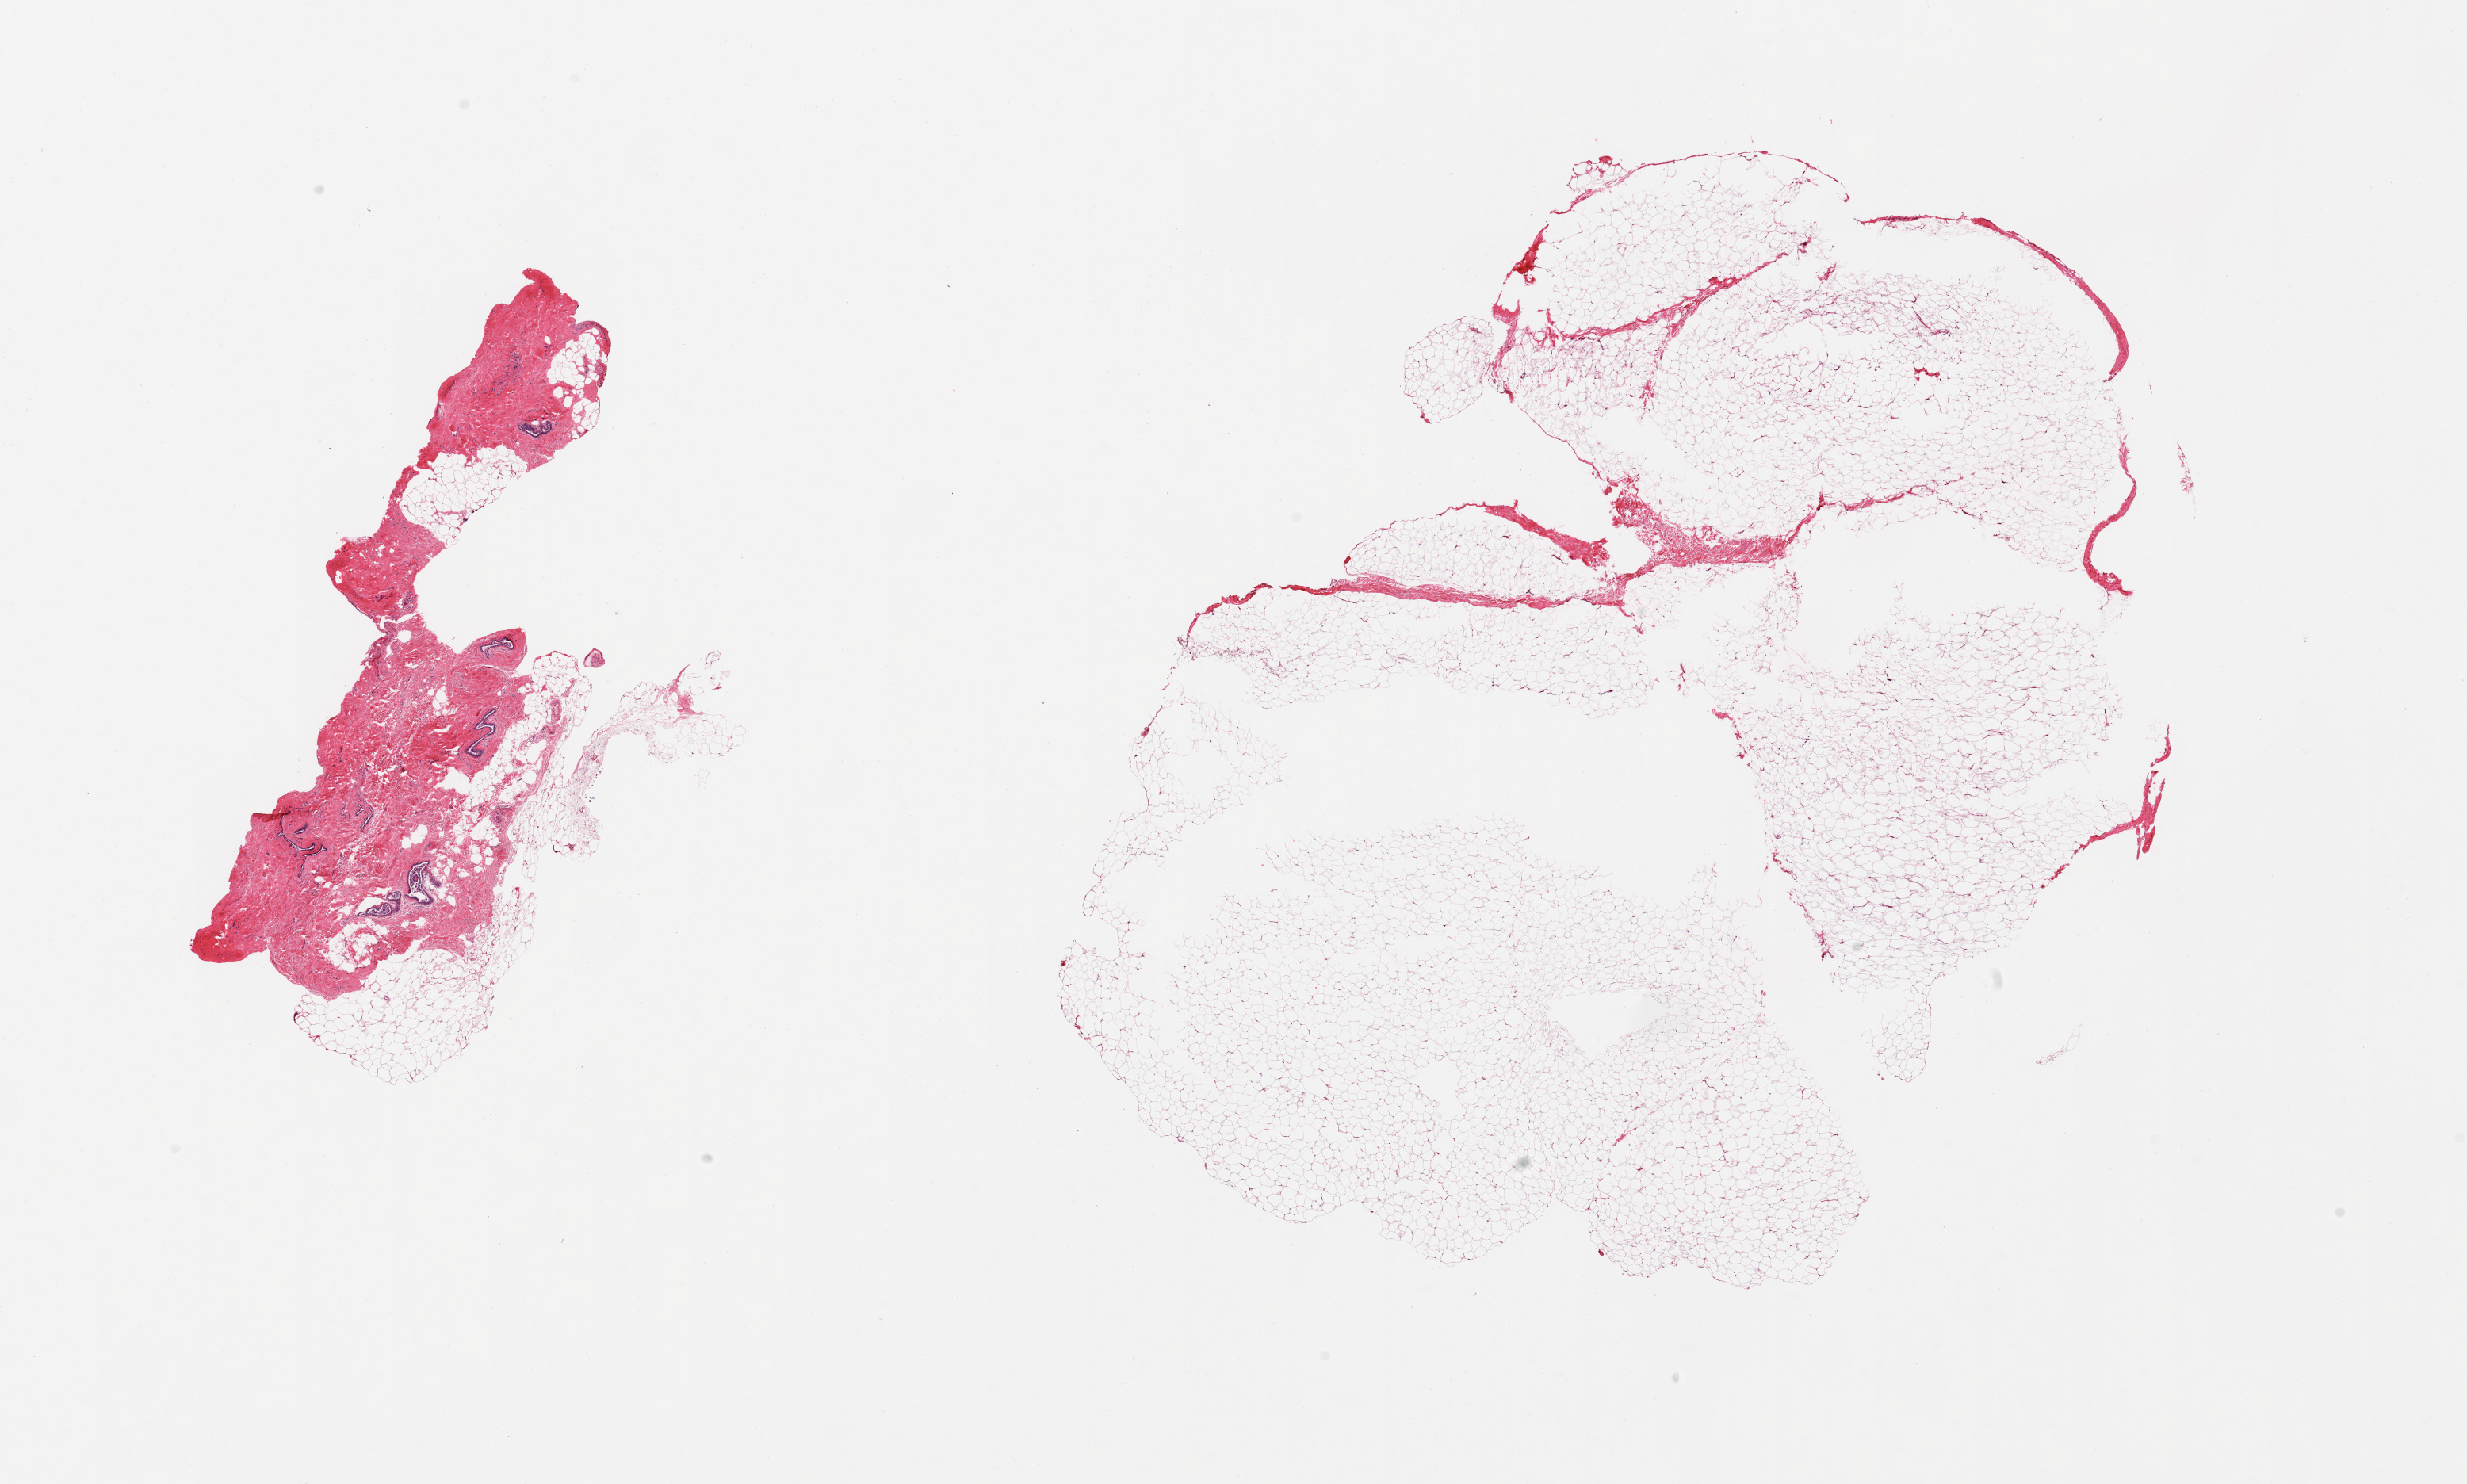
Hematoxylin and eosin (H&E) whole-slide image, whole scanned area (about 24.6 x 14.8 mm) shown as a low-resolution overview. PAXgene-fixed paraffin-embedded (PFPE) section. Section of breast (target tissue). Donor tissue sample. Donor sex: male.
Reviewer comment on this tissue sample: 2 pieces, mainly fibroadipose elements; a few ductal elements, rep delinetaed; focal gynecomastoid hyperplasia.